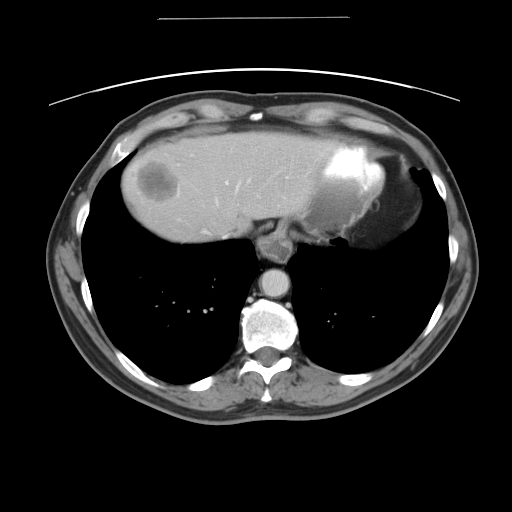
Contrast-enhanced abdominal CT, one axial slice. Position 41 of 49 along the scan axis. 120 kVp. Intravenous contrast given. Soft-tissue window (W 400 / L 40 HU). 512 × 512 image matrix, field of view 413 × 413 mm. Male patient, age 57 years. Case-level facts recorded for this patient, not image findings: diagnosis: colorectal cancer liver metastases, imaged before liver resection; multiple liver metastases: yes; largest metastasis: 4 cm; disease in both lobes: no.
Outlined on this slice (outlined manually by an expert reader):
- hepatic veins: bounding box [x1, y1, x2, y2] px = [202, 184, 238, 235]
- liver: [119, 132, 334, 243]
- planned liver remnant (the part of the liver to remain after resection): [205, 132, 334, 240]
- liver metastasis: [133, 158, 180, 203]